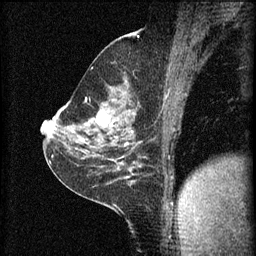
Breast MRI (dynamic contrast-enhanced), one sagittal slice; position 36 of 60 along the scan axis; 3 images stored at this slice position (order not interpretable as contrast timing); 1.5 T; TE 4.2 ms, TR 8.2 ms; 256 × 256 image matrix. Patient: female, 59 years.
Outlined on this slice (semi-automatic segmentation, software-assisted and operator-edited):
- analysis volume of interest (the breast-tissue region the enhancement analysis was run in; not a lesion): box from (x=78, y=92) to (x=137, y=135) px
- tumour enhancement mask (voxels above the 70 % enhancement threshold inside the analysis volume of interest): (x=96, y=110)–(x=111, y=127)